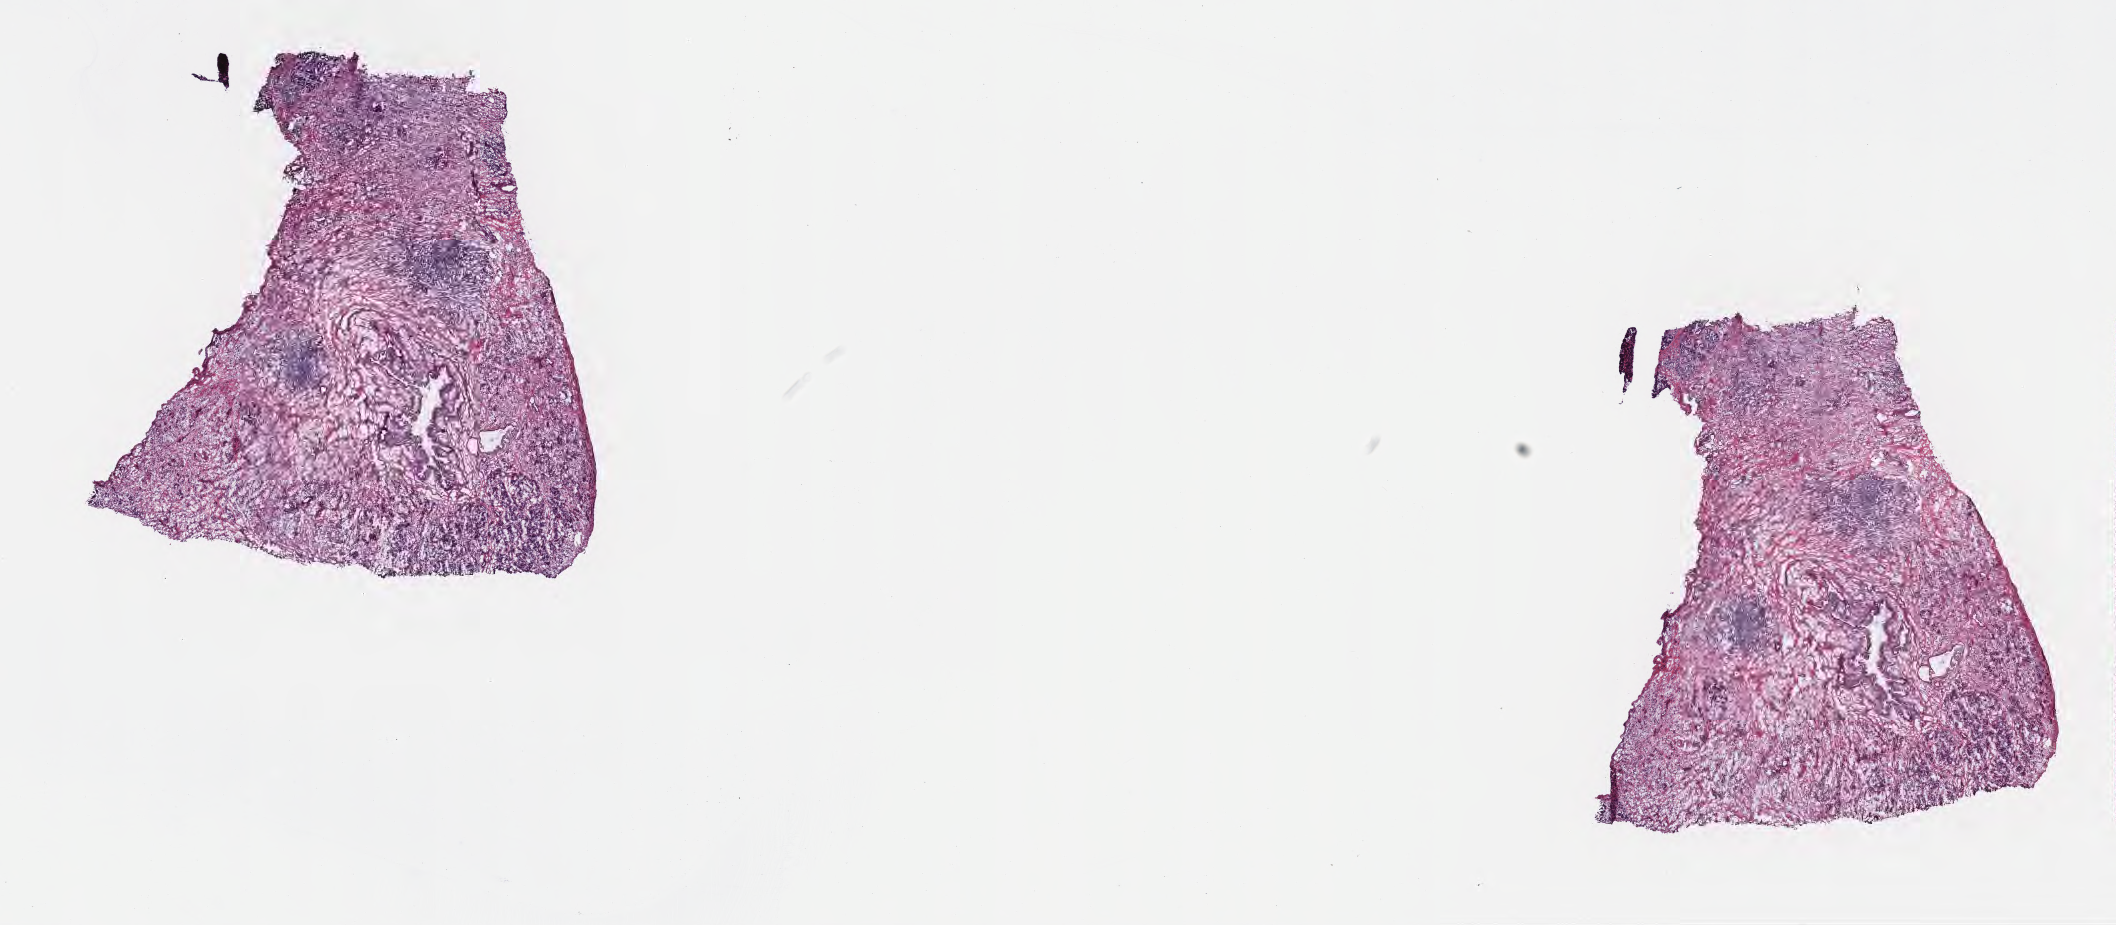
H&E whole-slide image, shown as a low-resolution overview of the whole scanned area (about 17.1 x 7.5 mm), frozen section, specimen: primary tumor, site: head of pancreas. Male, age 77 years at initial diagnosis. Tumor grade: G2 (moderately differentiated). Slide review estimates, as recorded: tumor cells 15%, tumor nuclei 80%, stromal cells 80%, necrosis 0%, normal cells 5%. Inflammatory infiltration, as recorded: lymphocyte infiltration 0%, monocyte infiltration 0%, neutrophil infiltration 0%.
• AJCC pathologic stage: Stage III
• diagnosis: Infiltrating duct carcinoma, NOS